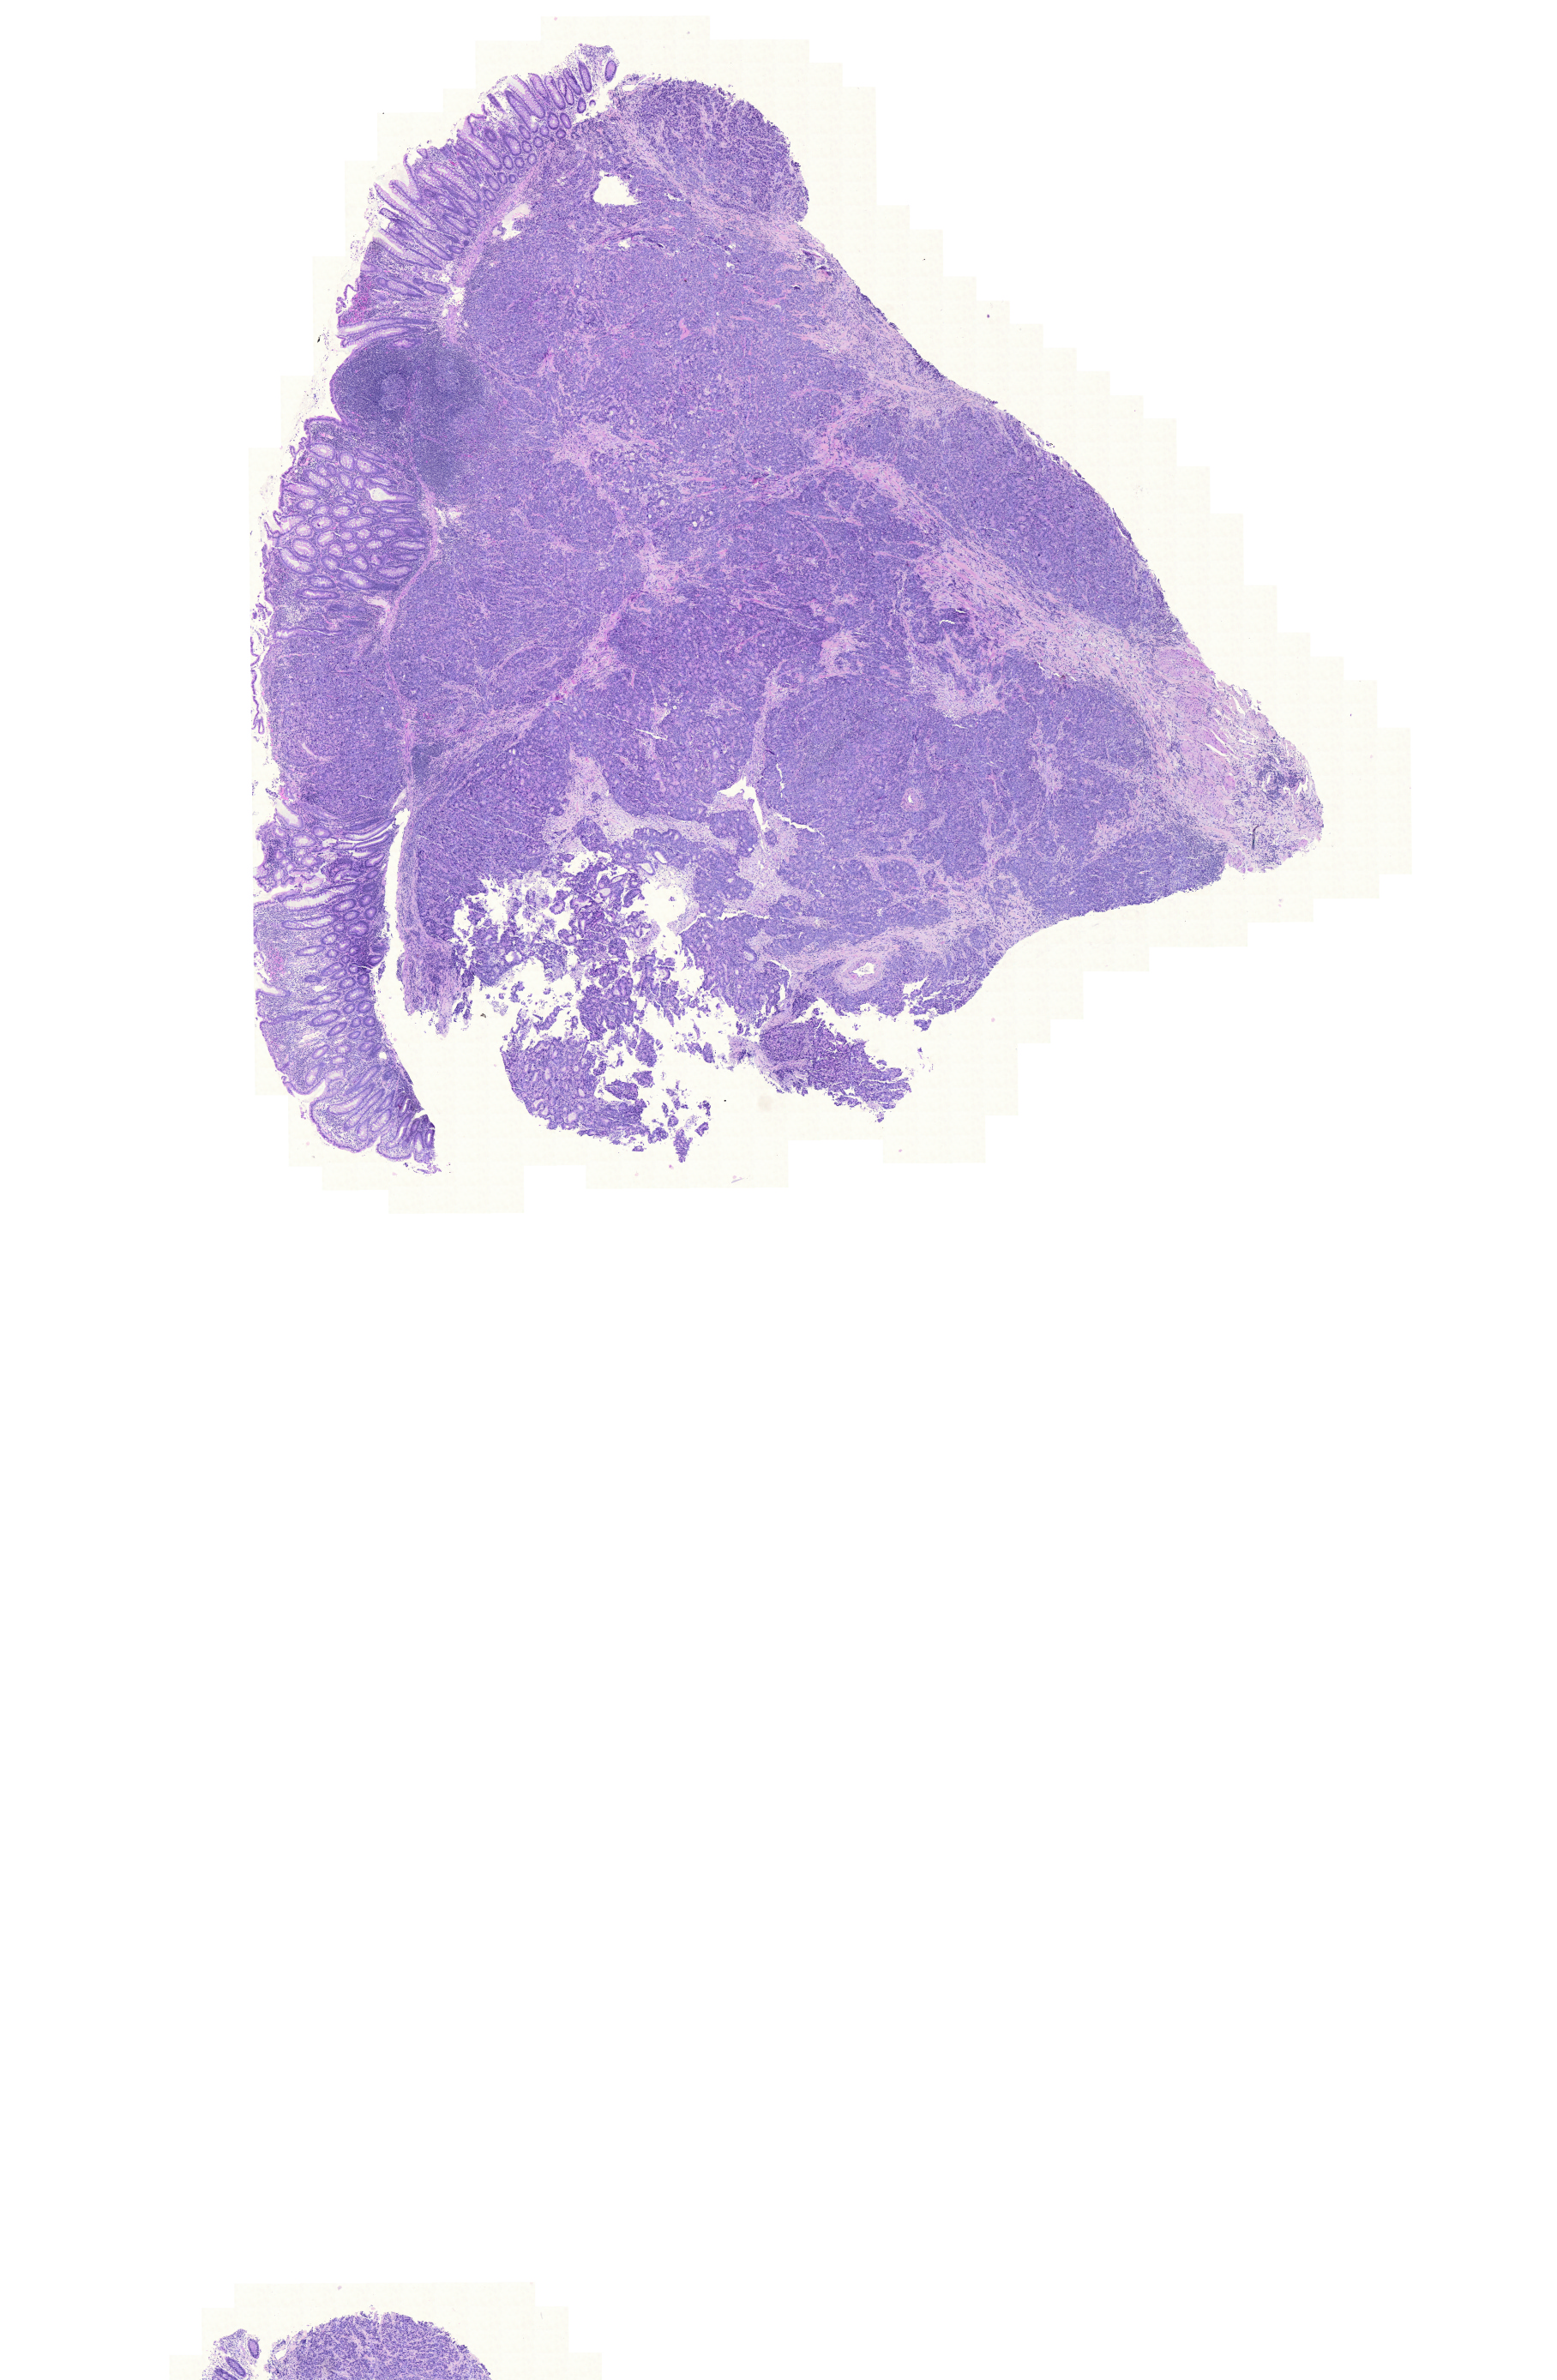
Digitized Hematoxylin and eosin (H&E) stained tissue section (whole slide) — a low-resolution overview of the entire scanned area, about 13.5 x 20.7 mm. Formalin-fixed paraffin-embedded (FFPE) diagnostic section. Colon, primary tumour sample. Female patient; age at initial diagnosis 88 years.
Lymph nodes positive (case pathology): 0 of 18 examined. AJCC pathologic stage: II (5th edition). Pathologic diagnosis: Adenocarcinoma, NOS.